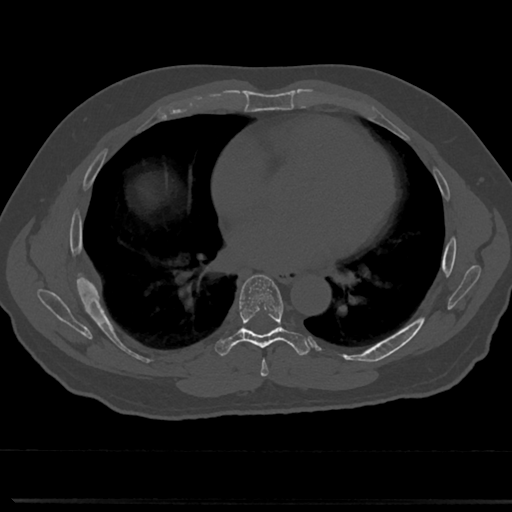
CT including the spine, one axial slice. Slice 409 of 817 in the series (ordered by position). Reconstruction kernel Br40s/3. Bone window (W 1800 / L 400 HU). 512 × 512 image matrix, field of view 355 × 355 mm. Patient: male, 61 years. Case-level facts recorded for this patient, not image findings: primary cancer: prostate.
Annotated regions visible in this slice (semi-automatic segmentation, software-assisted and operator-edited):
- T6 vertebra: box from (x=255, y=338) to (x=319, y=368) px
- T7 vertebra: (x=216, y=275)–(x=307, y=357)